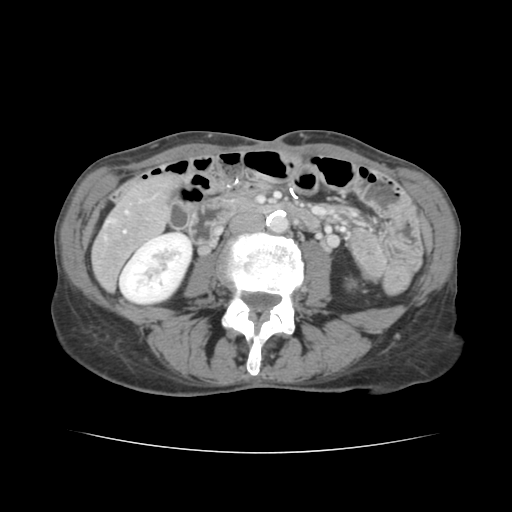
Contrast-enhanced abdominal CT, one axial slice; slice 33 of 136 in the series (ordered by position); 120 kVp; soft-tissue window (W 400 / L 40 HU); 512 × 512 image matrix. Female patient, age 77 years. Case-level facts recorded for this patient, not image findings: diagnosis: colorectal cancer liver metastases, imaged before liver resection; multiple liver metastases: yes; largest metastasis: 3 cm; disease in both lobes: no.
Outlined on this slice (manually delineated by an expert):
- hepatic veins: bounding box <109,211,127,222> (left, top, right, bottom; pixels)
- liver: <93,176,175,288>
- portal vein (with intrahepatic branches): <105,230,126,239>